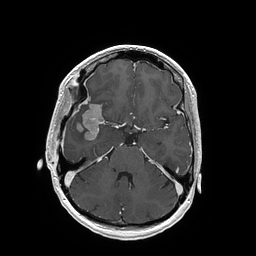
Brain MRI from a brain-tumour surgery series, one axial slice. Slice 112 of 202 in the series (ordered by position). T1-weighted post-contrast. 256 × 256 image matrix, field of view 250 × 250 mm. Case-level facts recorded for this patient, not image findings: histopathology: Glioblastoma; WHO grade: 4; IDH mutation: no; tumour location: Right Insular.
Annotated regions visible in this slice (manually delineated by an expert):
- tumour: bounding box [x1, y1, x2, y2] px = [76, 104, 103, 141]